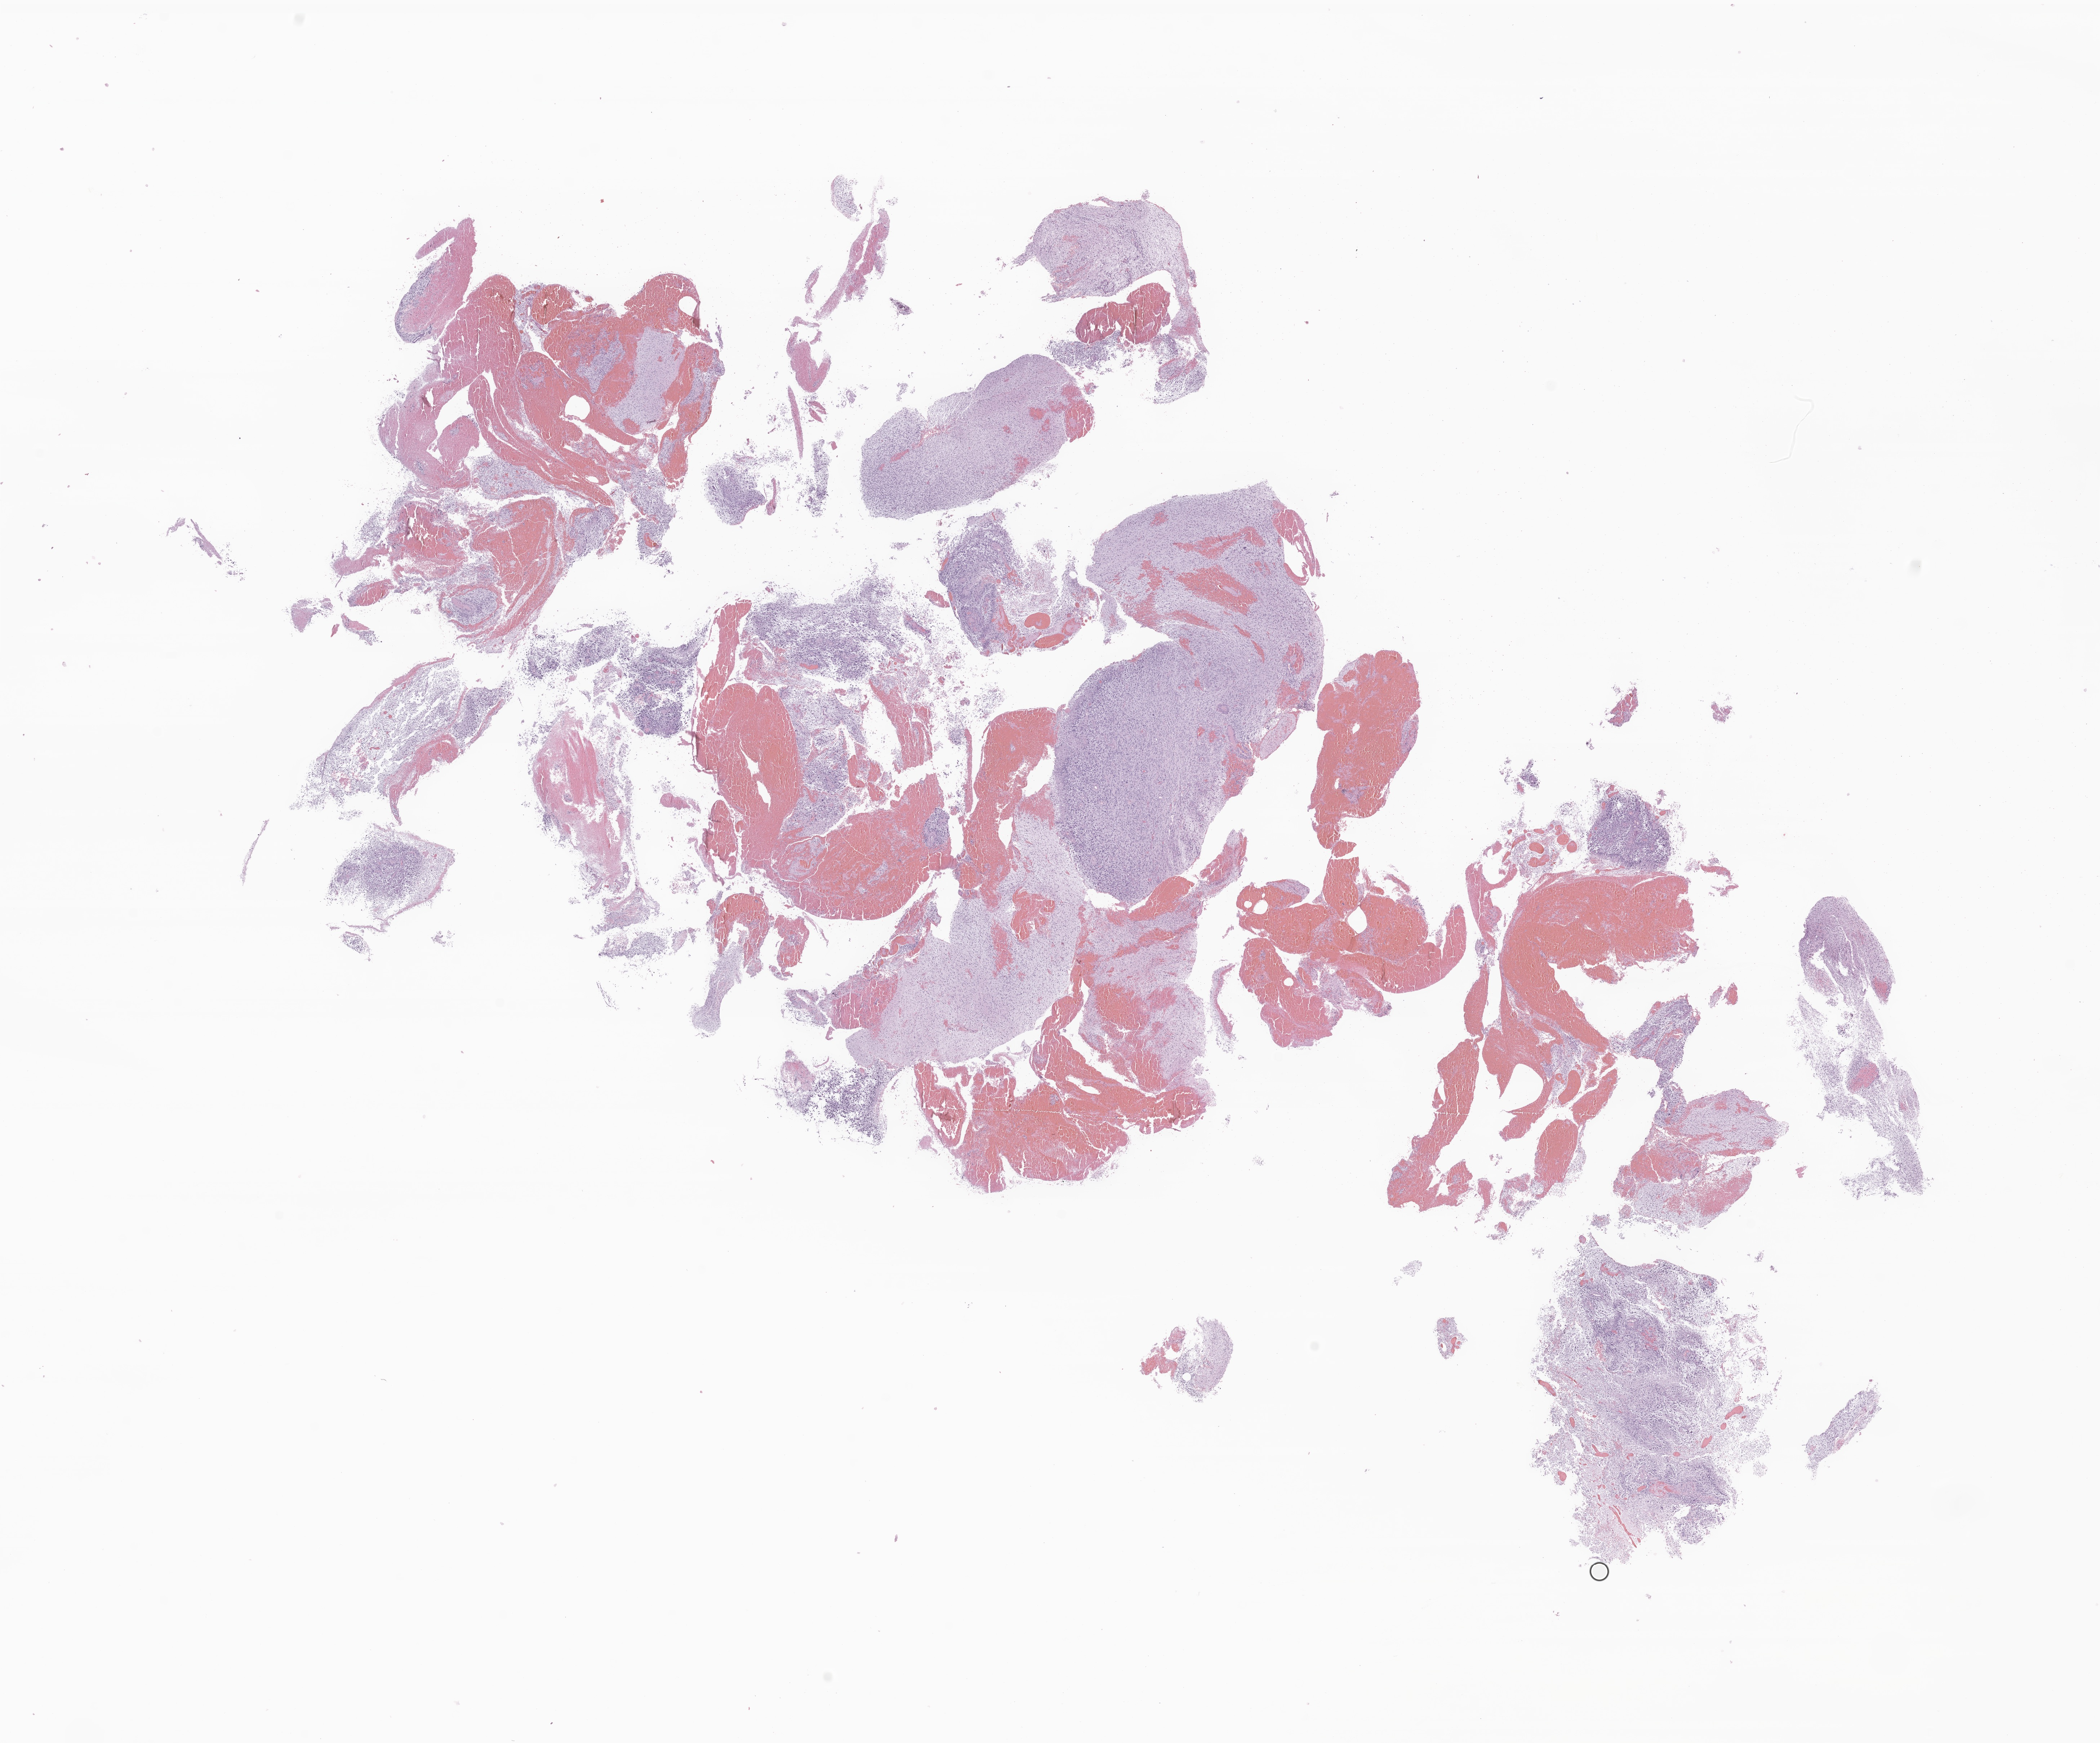
Digitized hematoxylin and eosin (H&E)-stained section of tumor tissue from the brain stem — low-resolution overview of the scanned area, about 24.6 x 20.4 mm. Formalin-fixed paraffin-embedded section. Patient male; age 67 months.
• diagnosis (ICD-O-3 morphology term): Glioma, malignant